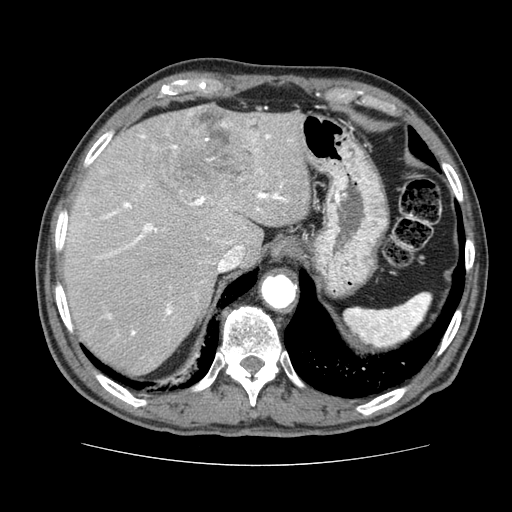
Contrast-enhanced abdominal CT (liver protocol), one axial slice; position 57 of 79 along the scan axis; reconstruction kernel STANDARD; 120 kVp; soft-tissue window (W 400 / L 40 HU); 512 × 512 image matrix. Case-level facts recorded for this patient, not image findings: diagnosis: hepatocellular carcinoma (patient treated with transarterial chemoembolisation; whether this scan precedes or follows treatment is not stated here); TNM stage (as recorded): Stage-I; Child-Pugh class: A.
Structures marked on this image (semi-automatically segmented with operator editing):
- liver parenchyma outside the tumour (the mass and vessels are separate outlines, so this box may not span the whole liver): box from (x=62, y=106) to (x=310, y=375) px
- mass: (x=142, y=106)–(x=257, y=206)
- liver vessels: (x=86, y=134)–(x=292, y=335)